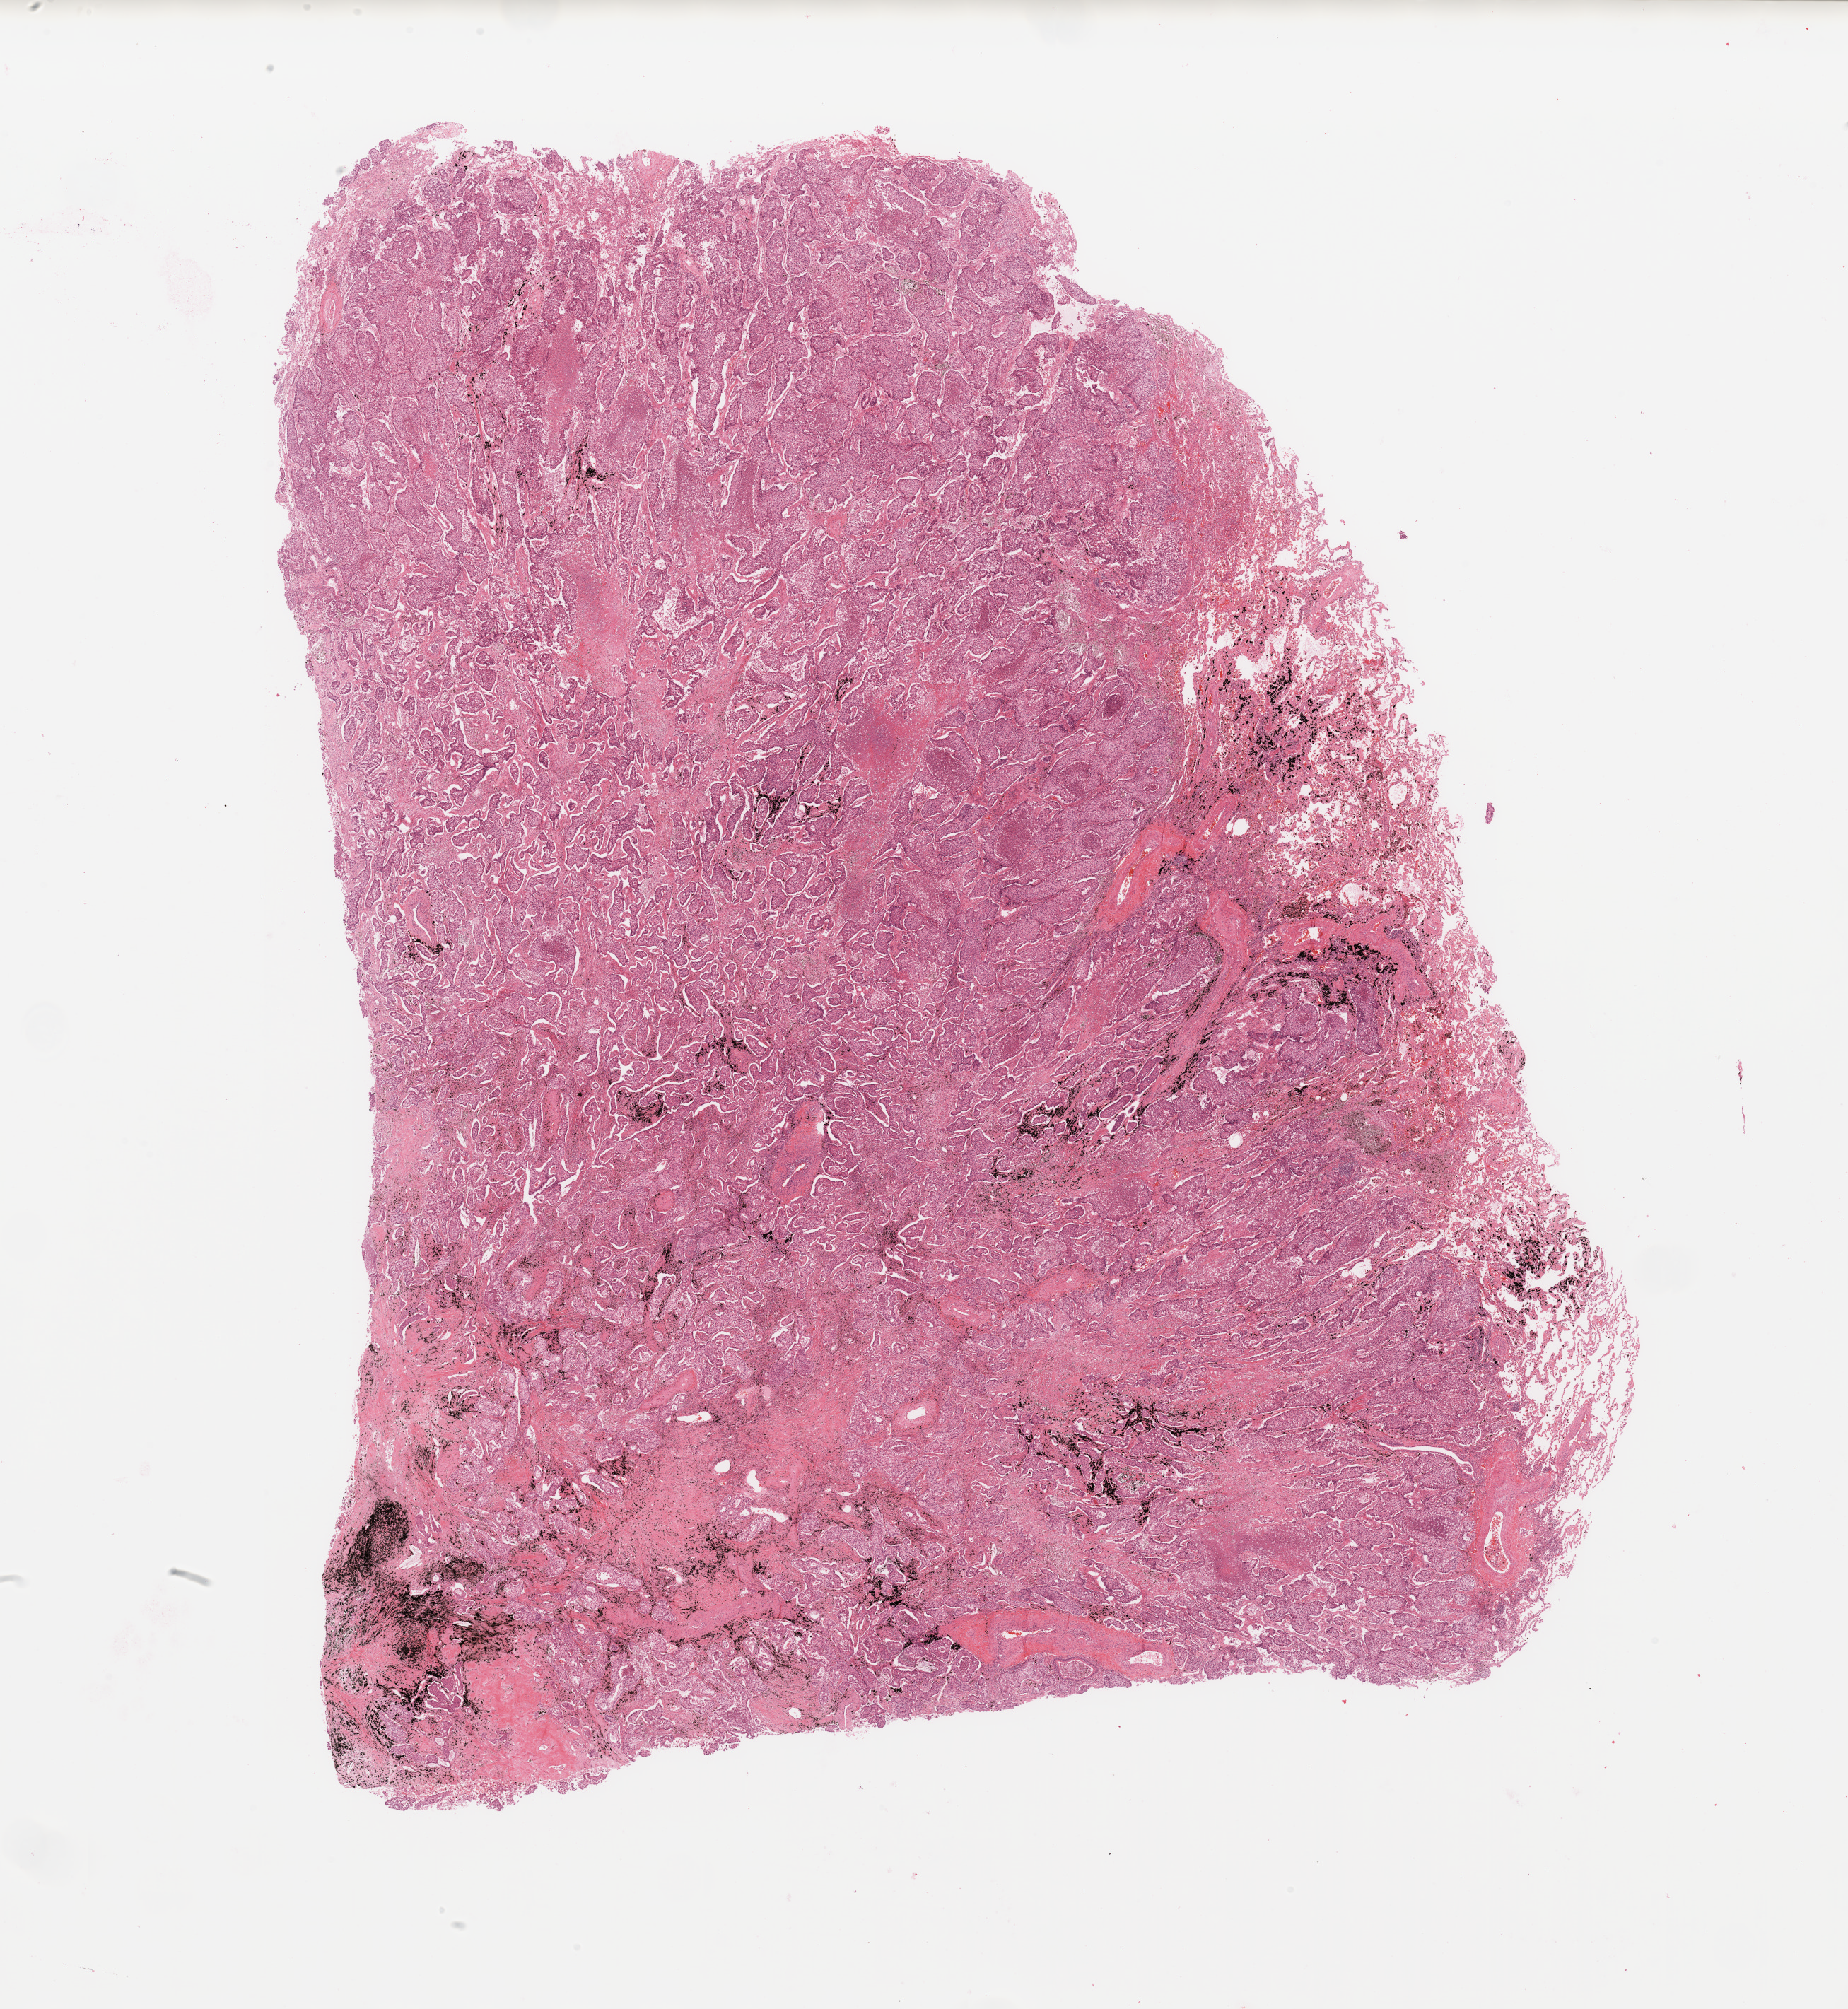
Whole-slide histology image, H&E — shown as a low-resolution overview of the whole scanned area (about 20.7 x 22.5 mm, acquisition: 20x scan), lung, tumour tissue. Male, 64 y/o.
Histologic diagnosis: Adenocarcinoma, NOS.